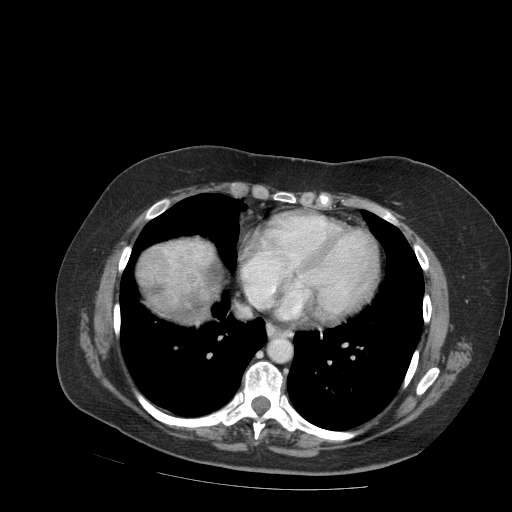
Contrast-enhanced abdominal CT (liver protocol), one axial slice. Position 89 of 99 along the scan axis. 140 kVp. Soft-tissue window (W 400 / L 40 HU). 512 × 512 image matrix. Case-level facts recorded for this patient, not image findings: diagnosis: hepatocellular carcinoma (patient treated with transarterial chemoembolisation; whether this scan precedes or follows treatment is not stated here); TNM stage (as recorded): Stage-IVB; Child-Pugh class: A; tumour differentiation: moderately differentiated; tumour nodularity: uninodular.
Annotated regions visible in this slice (semi-automatically segmented with operator editing):
- liver parenchyma outside the tumour (the mass and vessels are separate outlines, so this box may not span the whole liver): bounding box (x1, y1, x2, y2) in pixels: (136, 238, 214, 323)
- mass: (138, 243, 227, 323)